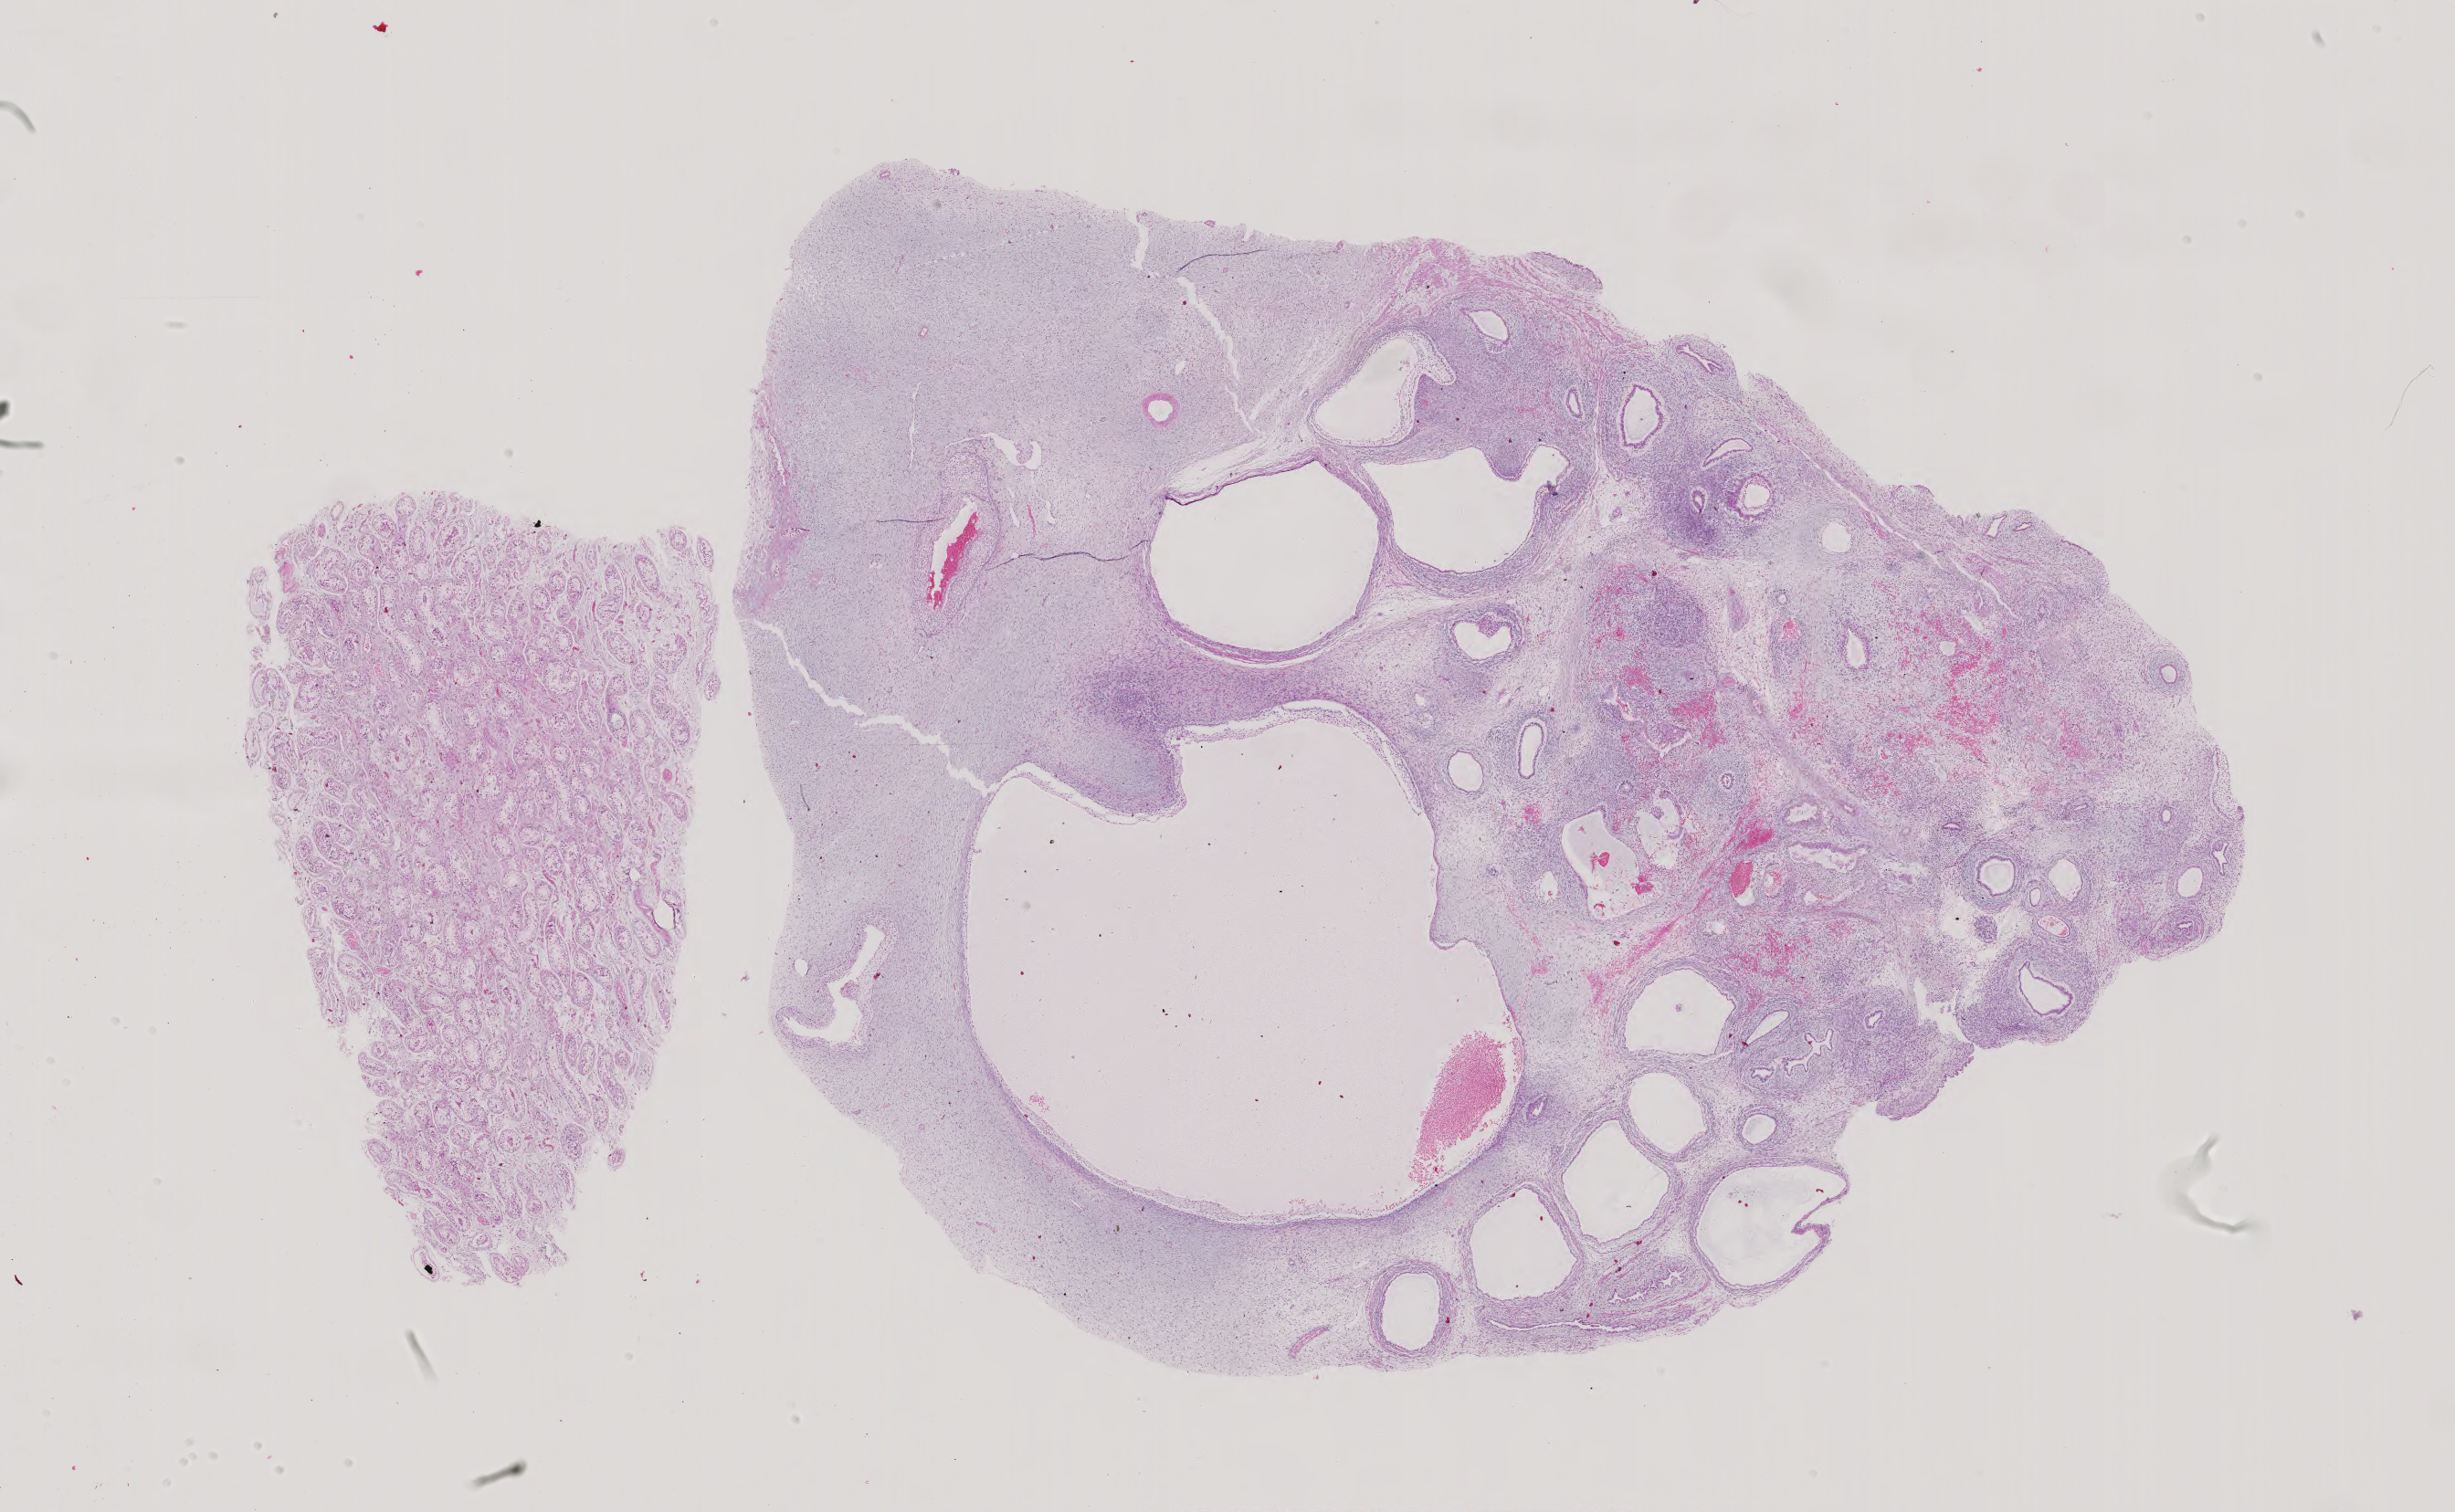
Whole-slide histology image, Hematoxylin and eosin (H&E) stained, shown as a low-resolution overview of the whole scanned area (about 19.6 x 12.1 mm, acquisition: 40x scan). Formalin-fixed paraffin-embedded (FFPE) diagnostic section. Primary tumour sample from the testis. Patient: male, age at initial diagnosis 22 years.
Diagnosis: Teratoma, benign.